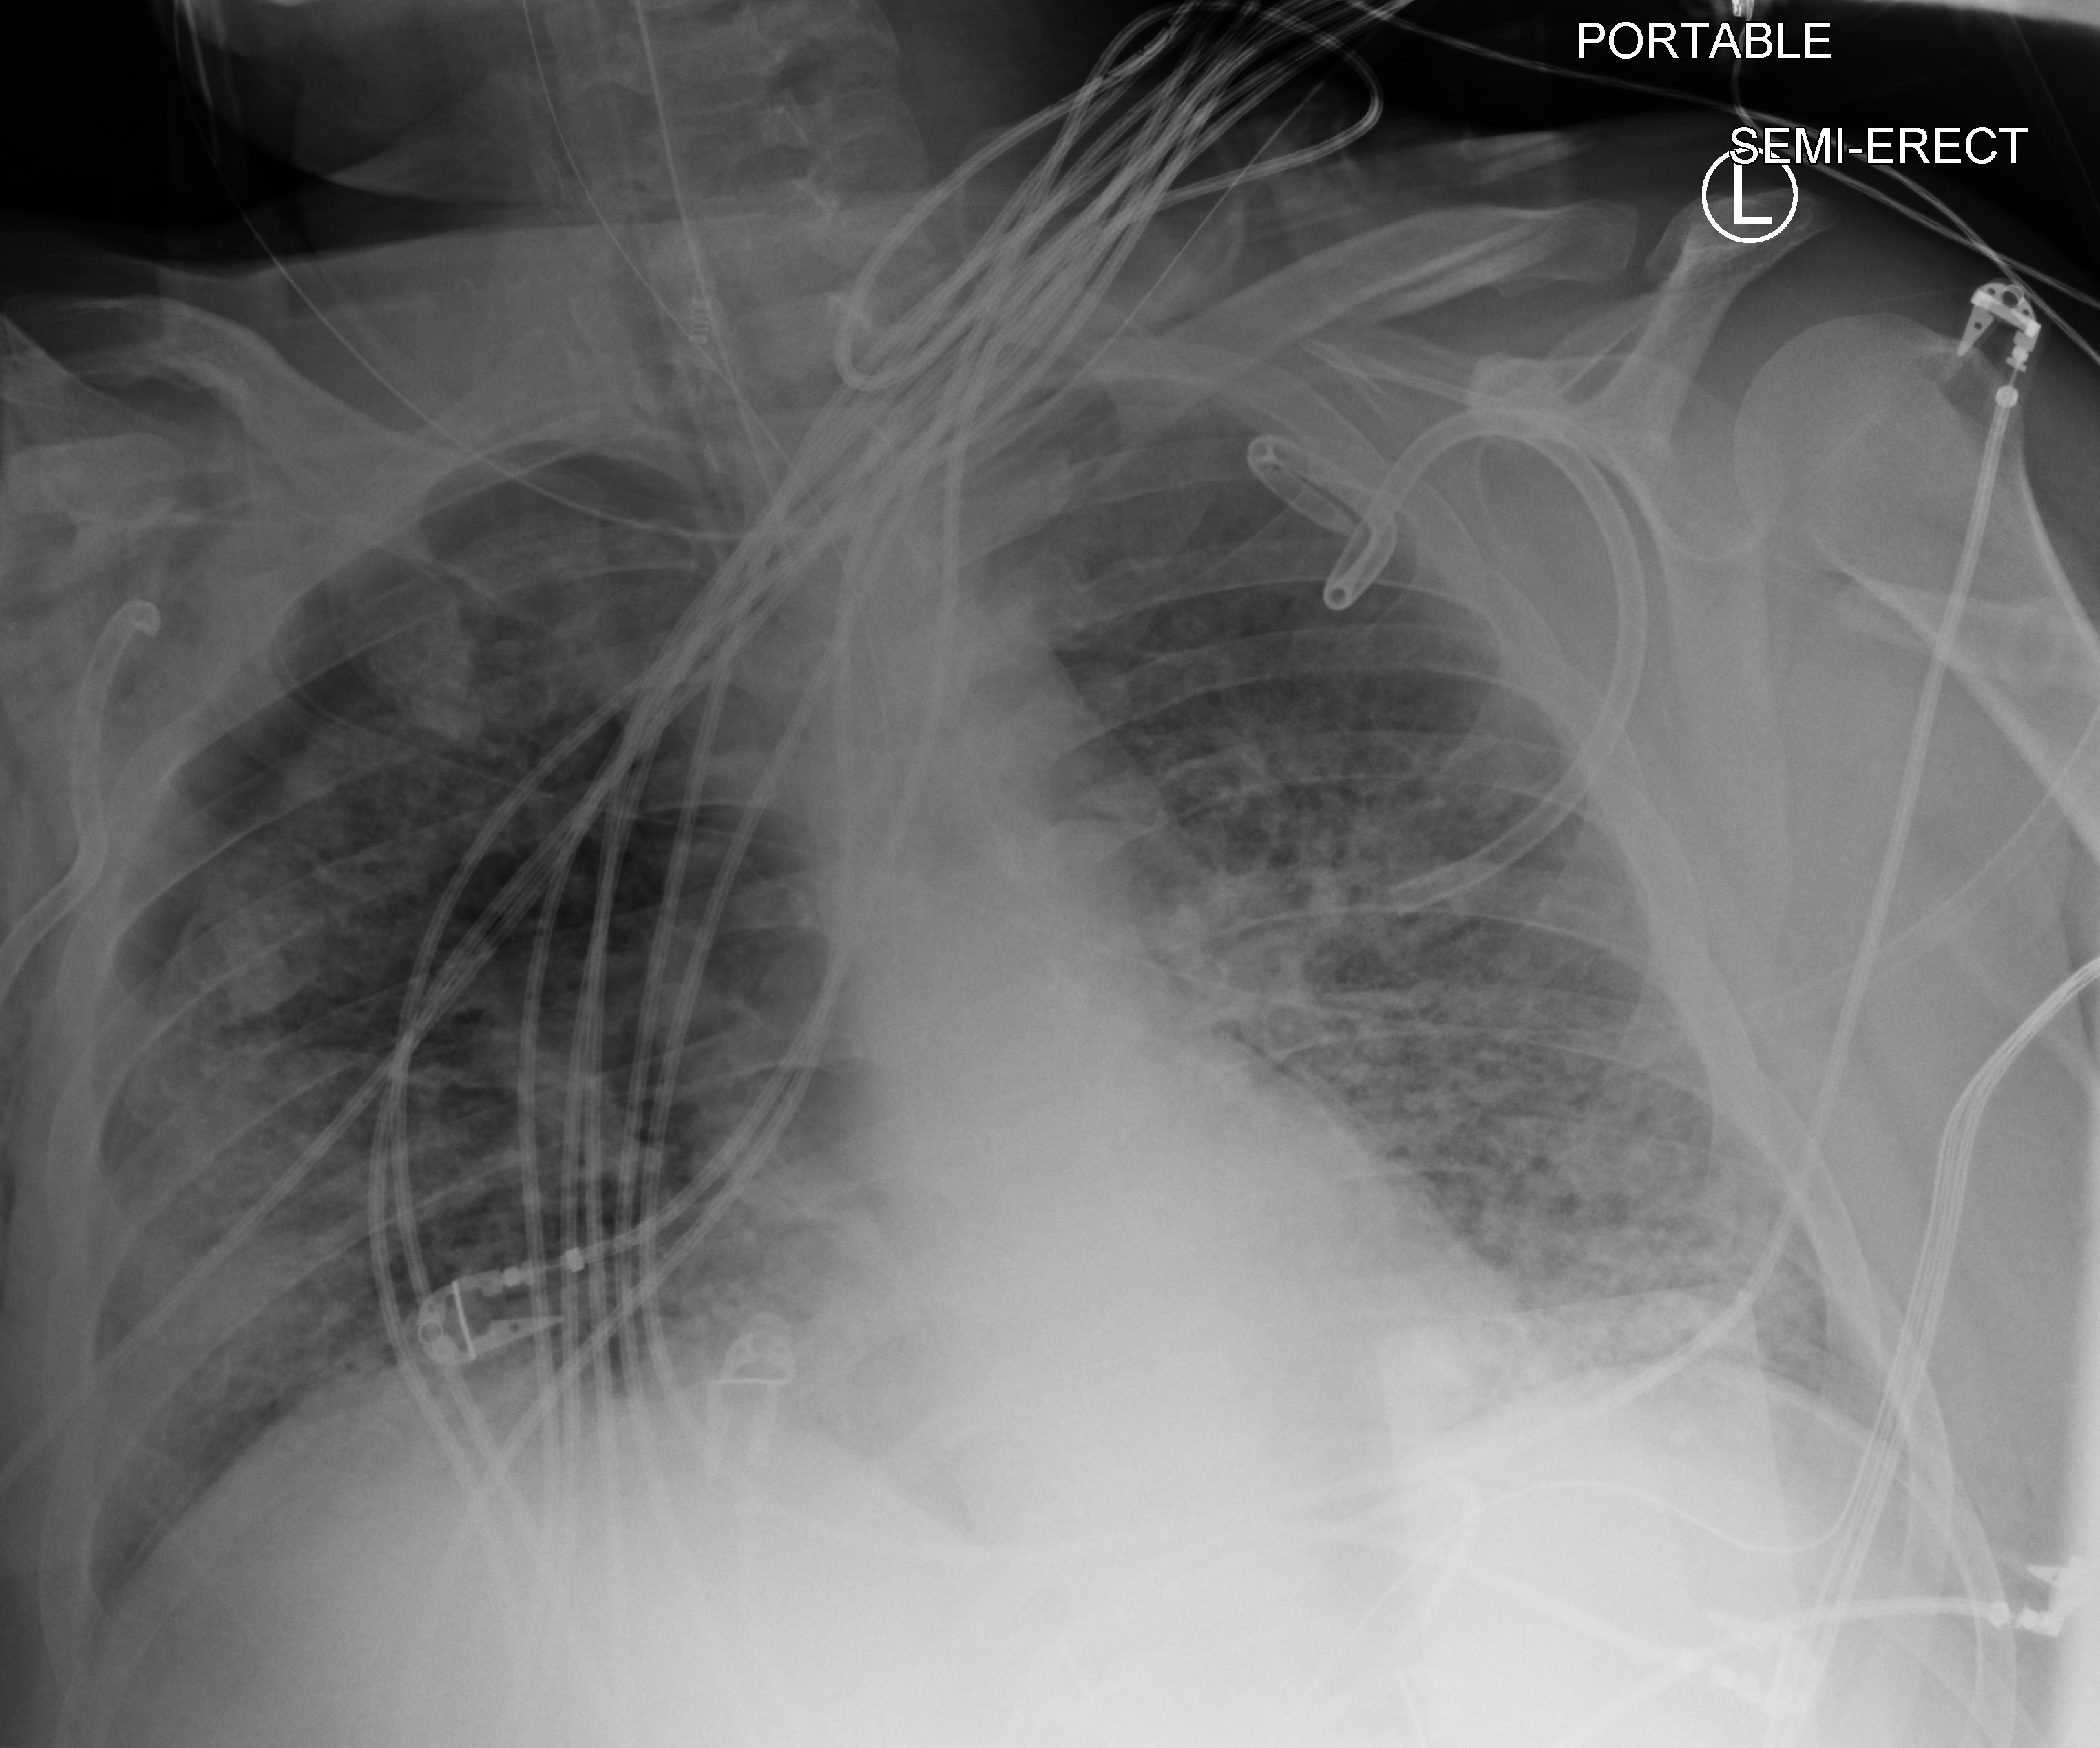
Chest X-ray (portable), anteroposterior (AP) projection. Patient hospitalised with COVID-19, aged 18–59 years.
From the hospital-stay record, not from the radiograph (when in the stay this image was taken is not recorded):
- mechanically ventilated during this hospital stay: yes
- admitted to intensive care during this hospital stay: yes